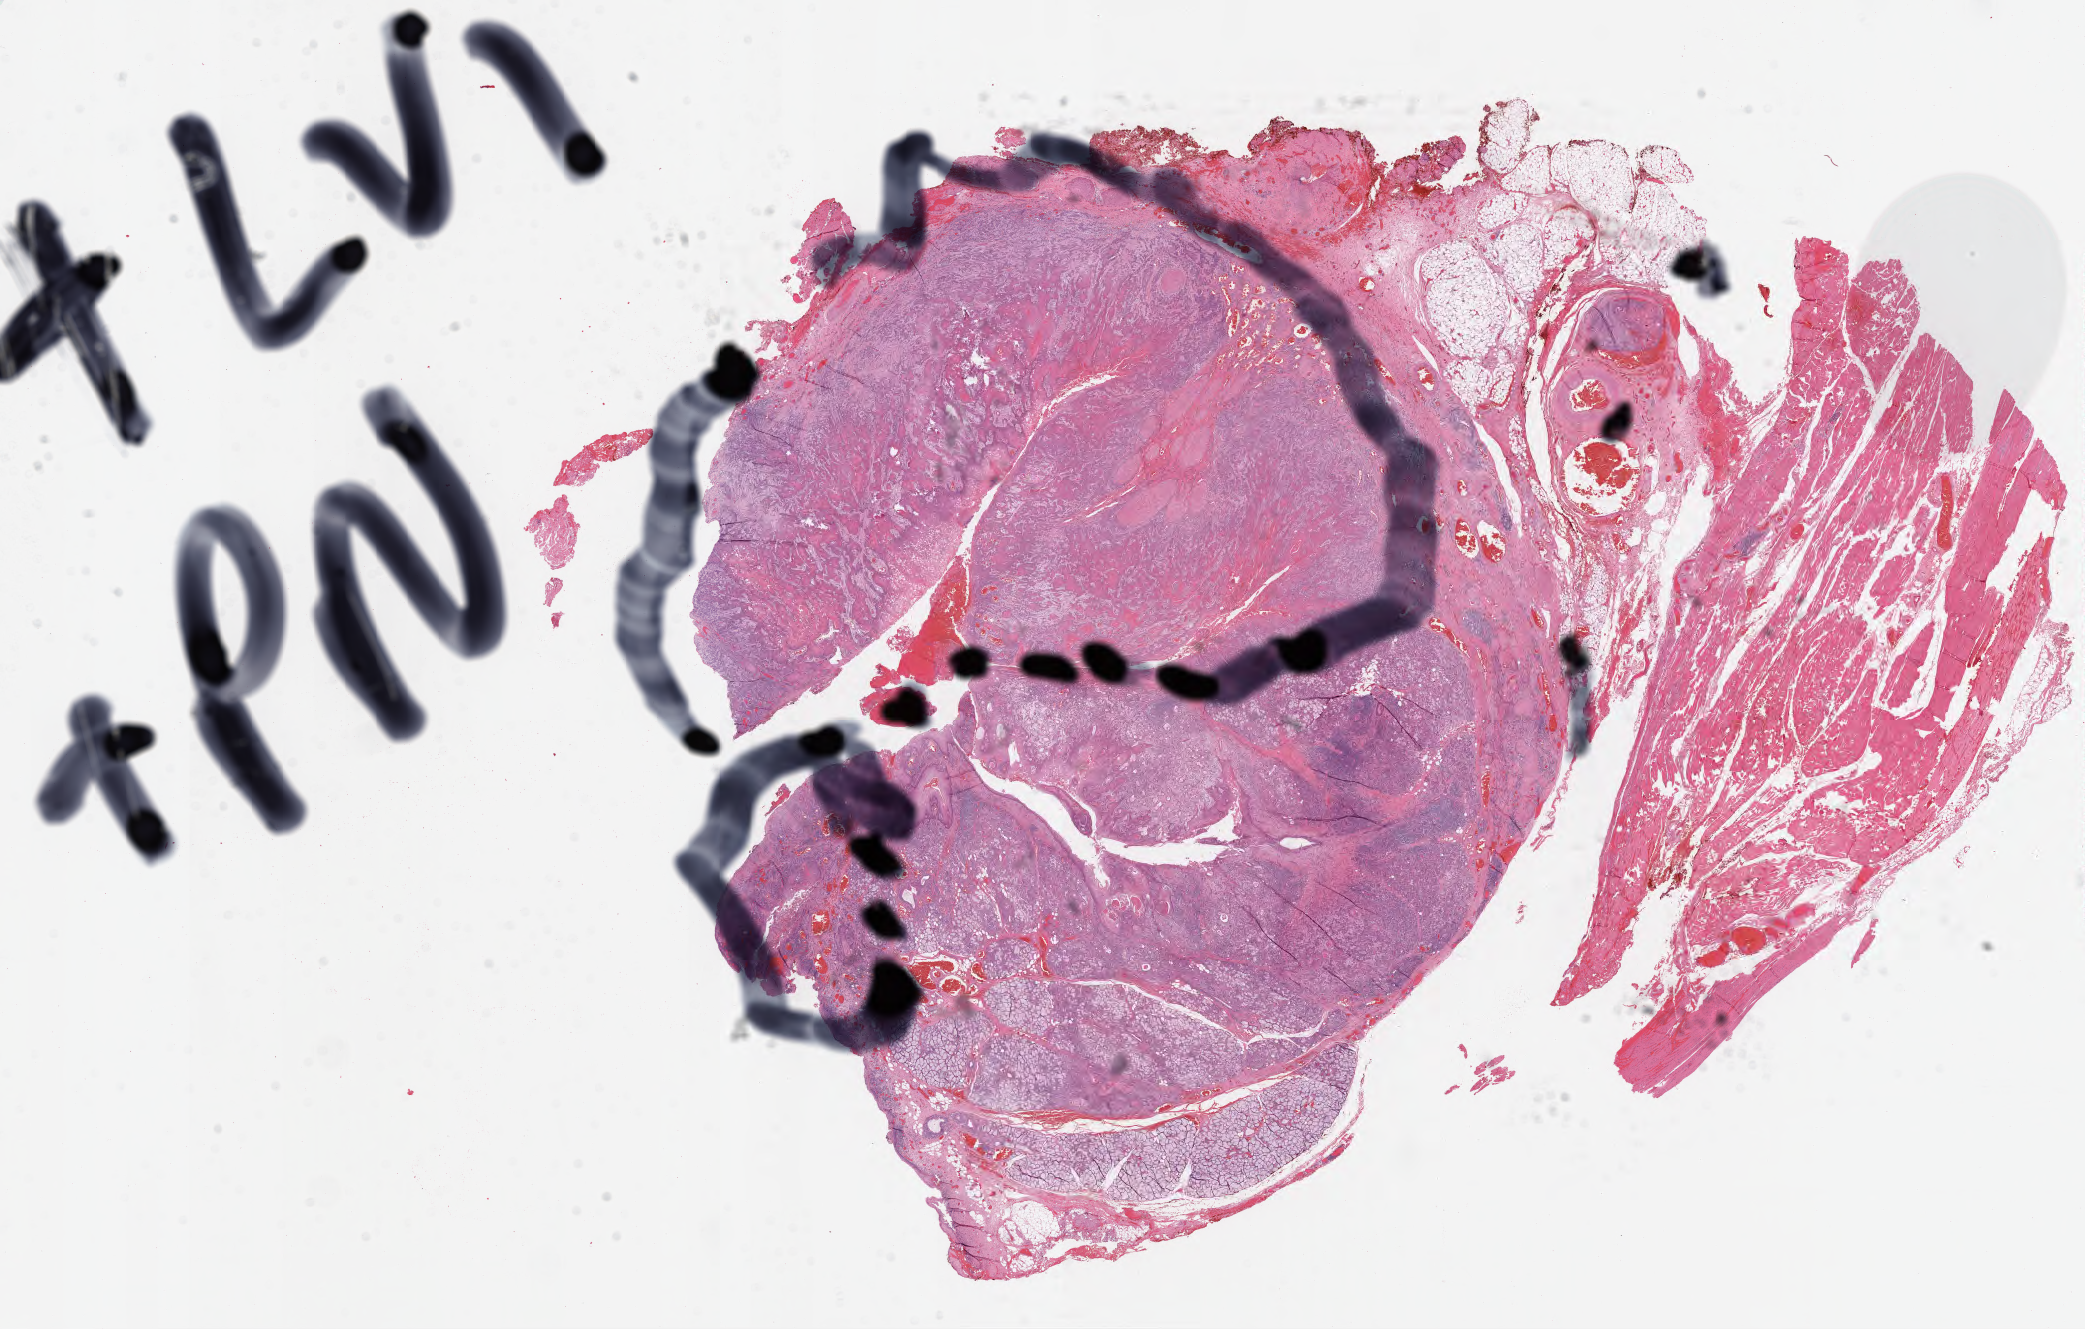
Whole-slide histology image, Hematoxylin and eosin (H&E) stained, shown as a low-resolution overview of the whole scanned area (about 32.8 x 20.9 mm, acquisition: 40x scan); FFPE section; head and neck, primary tumour sample. Male patient; age at initial diagnosis 55 years. Histologic grade: G2 (moderately differentiated).
• diagnosis: Squamous cell carcinoma, NOS (floor of mouth, NOS)
• lymph nodes positive (case pathology): 2 of 47 examined
• AJCC pathologic stage: IVA (6th edition)